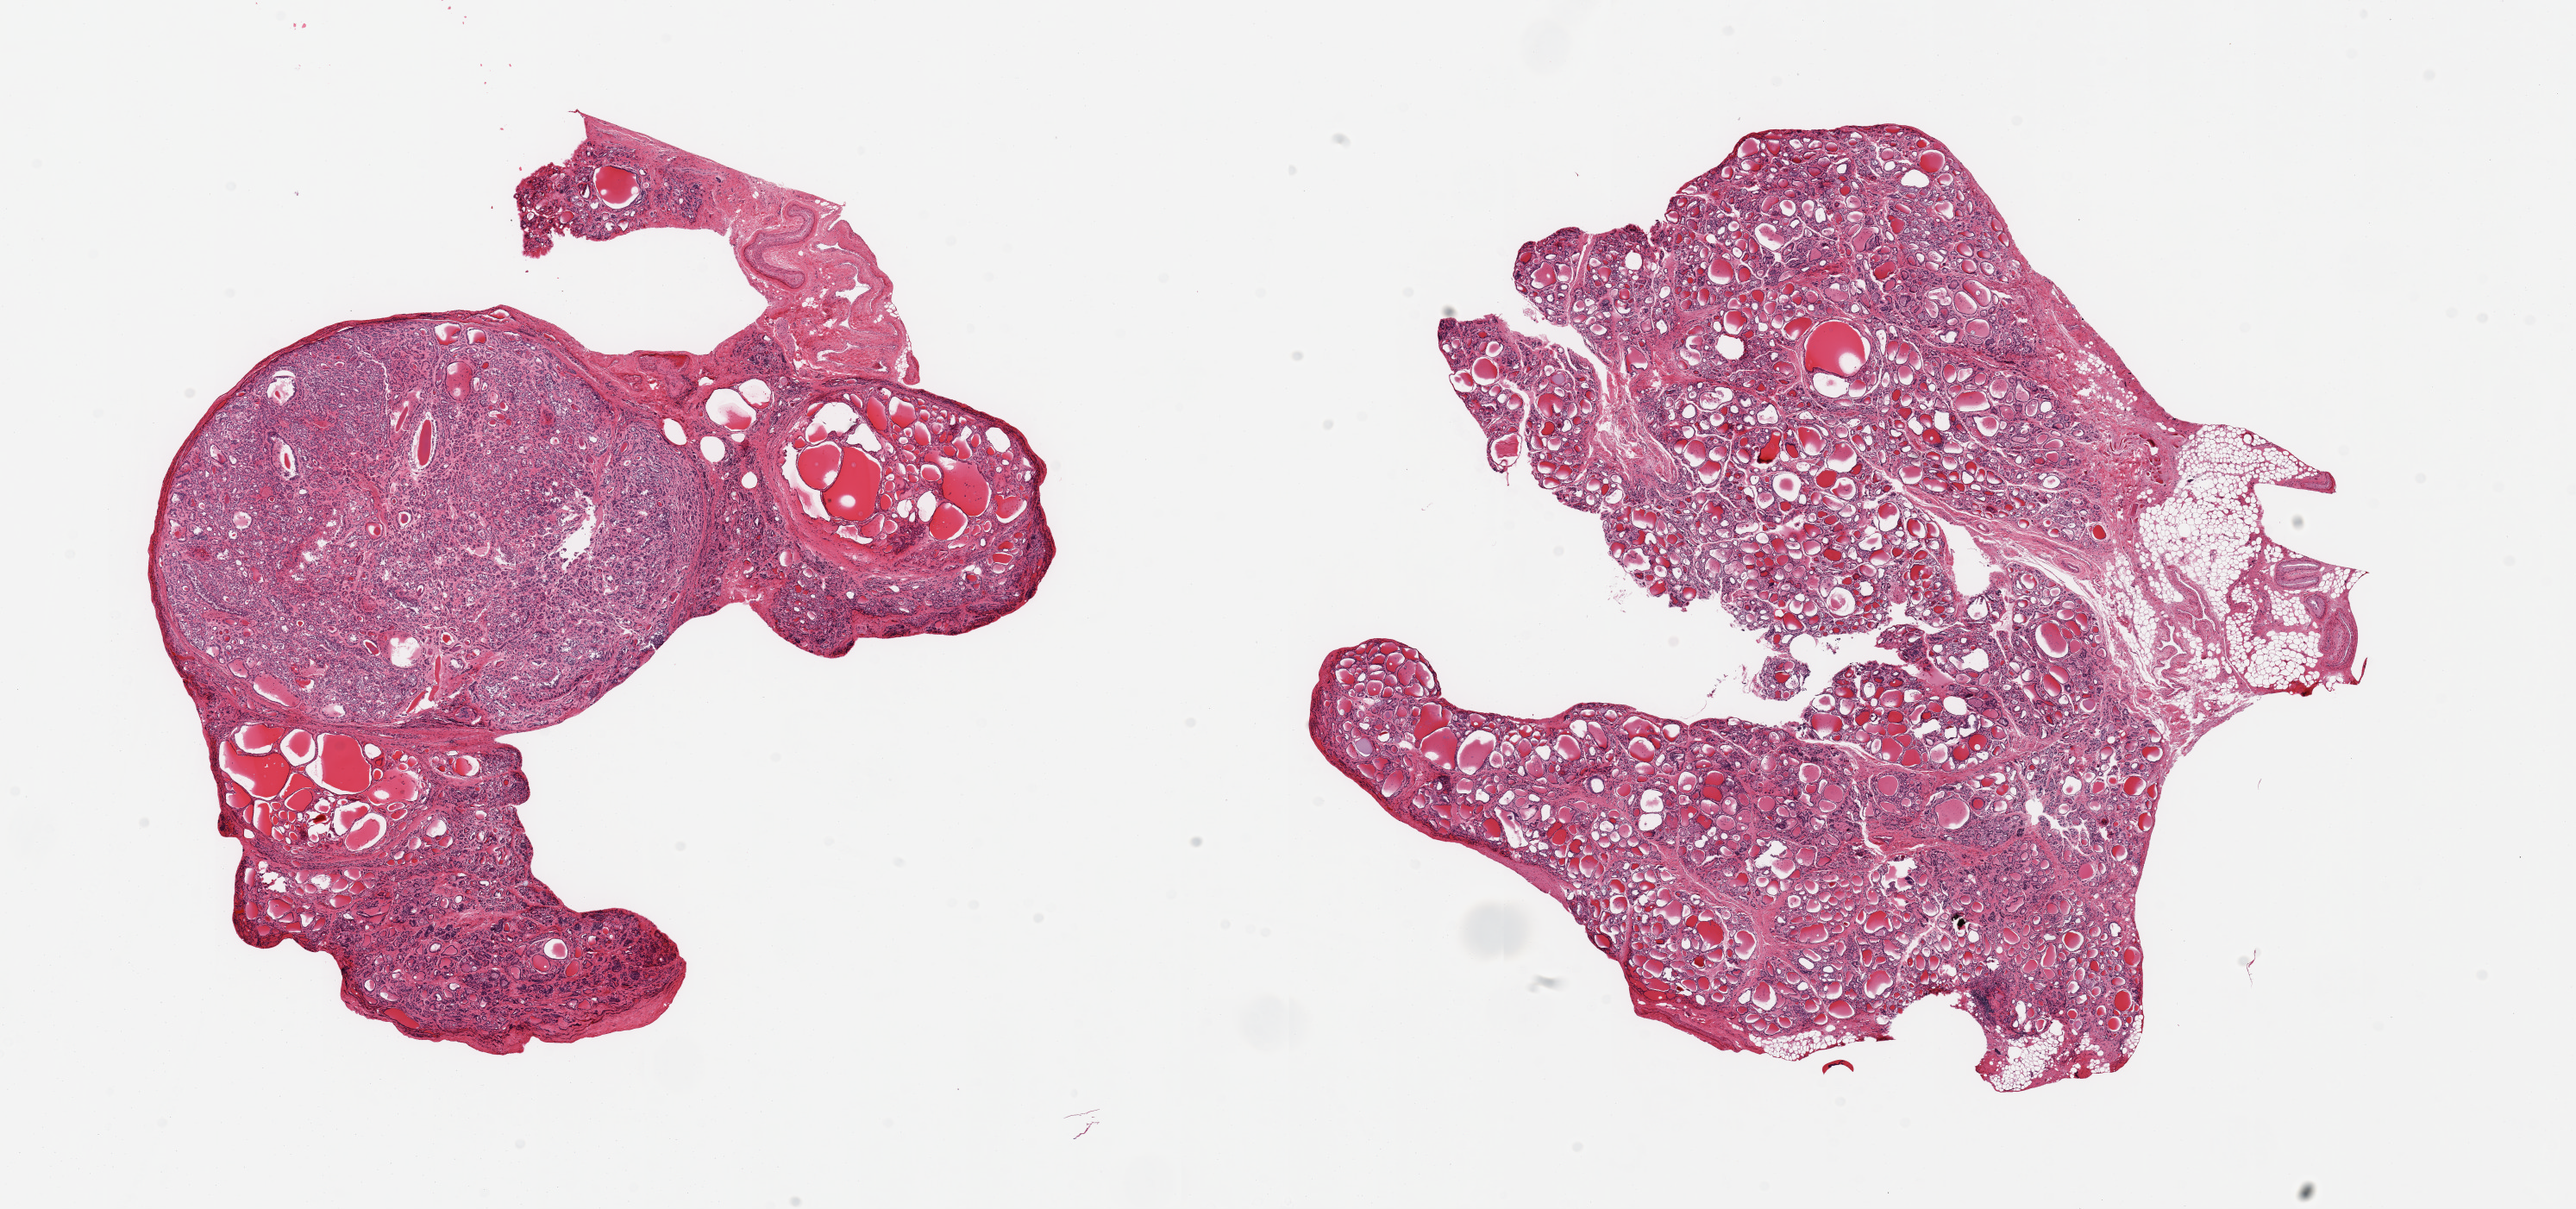
Hematoxylin and eosin (H&E) whole-slide image, brightfield — low-resolution overview of the scanned area, about 23.6 x 11.1 mm (acquisition: 20x scan). PAXgene-fixed, paraffin-embedded tissue. Sampled site (target tissue): thyroid. Donor tissue sample. Donor: female.
Pathologist's review note for this sample: 2 pieces, multinodular goiter, adenomatoid nodules up to ~5mm.